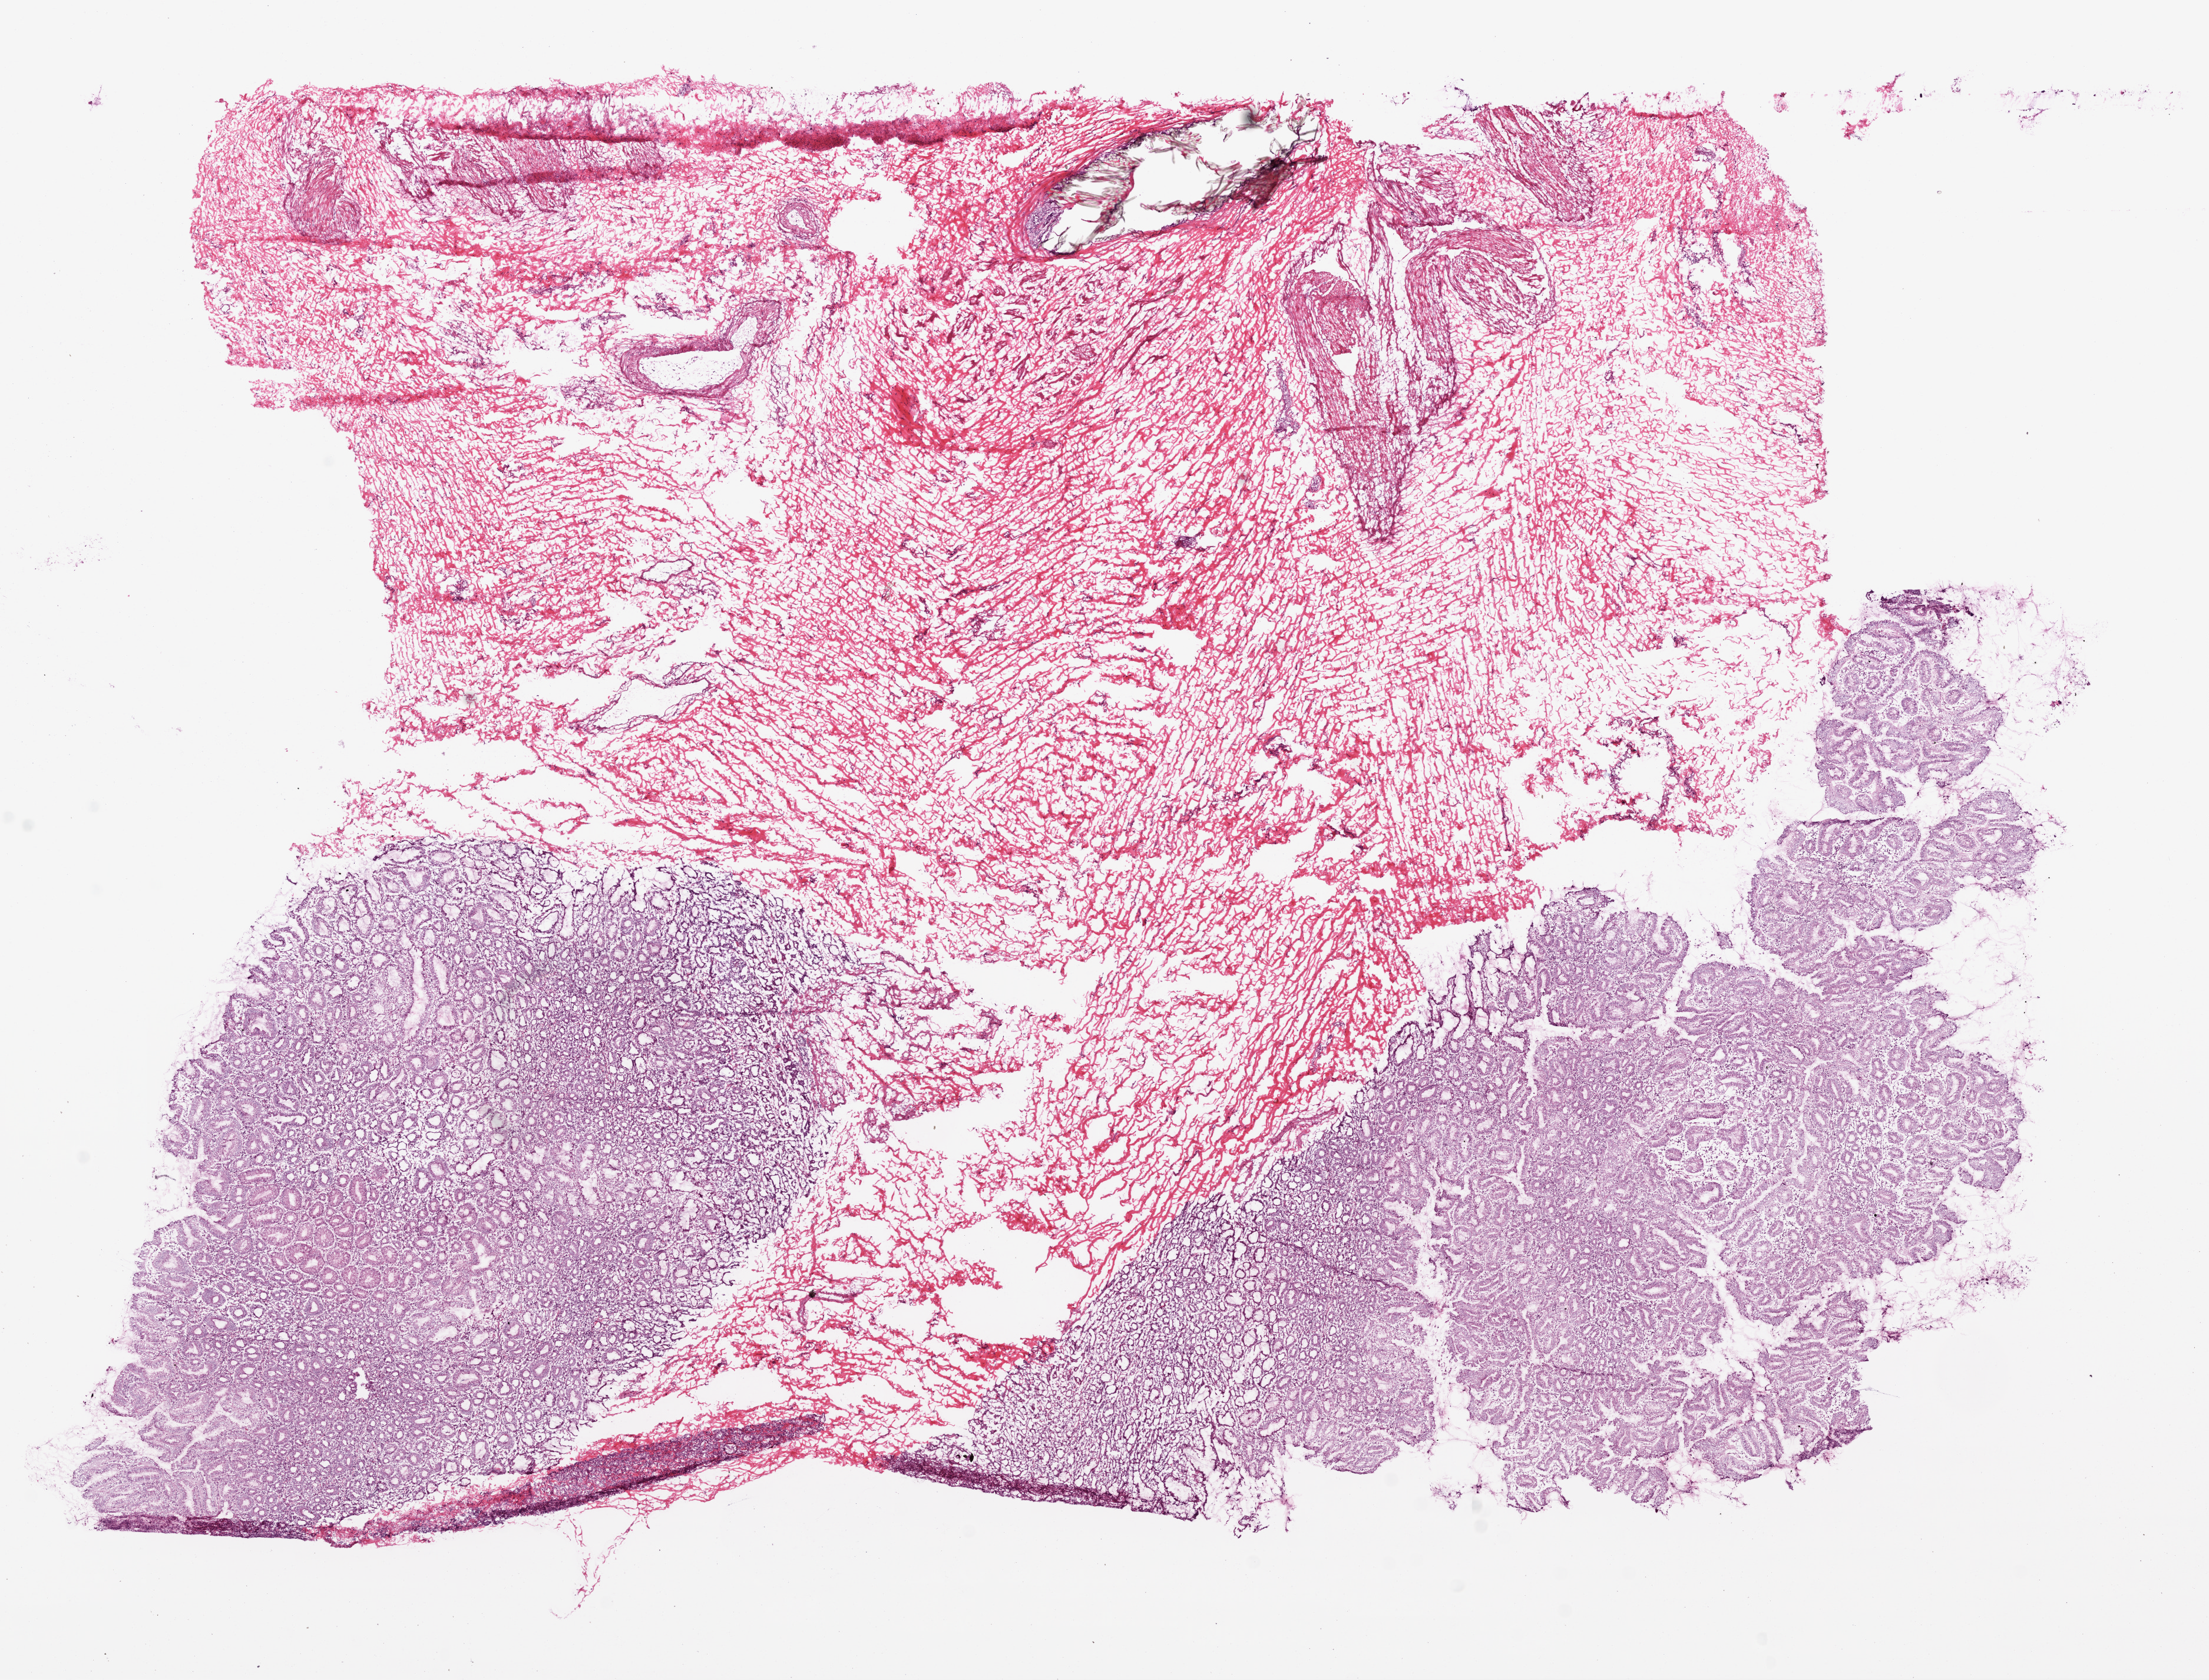
Digitized Hematoxylin and eosin (H&E) stained tissue section (whole slide) — whole scanned area (about 15.0 x 11.4 mm, acquisition: 20x scan) shown as a low-resolution overview; frozen section; sample: solid tissue normal (non-tumour tissue), stomach. Male, age 43 years at initial diagnosis.
• this section: solid tissue normal (non-tumour) sample from the same patient
• patient diagnosis: Adenocarcinoma, NOS